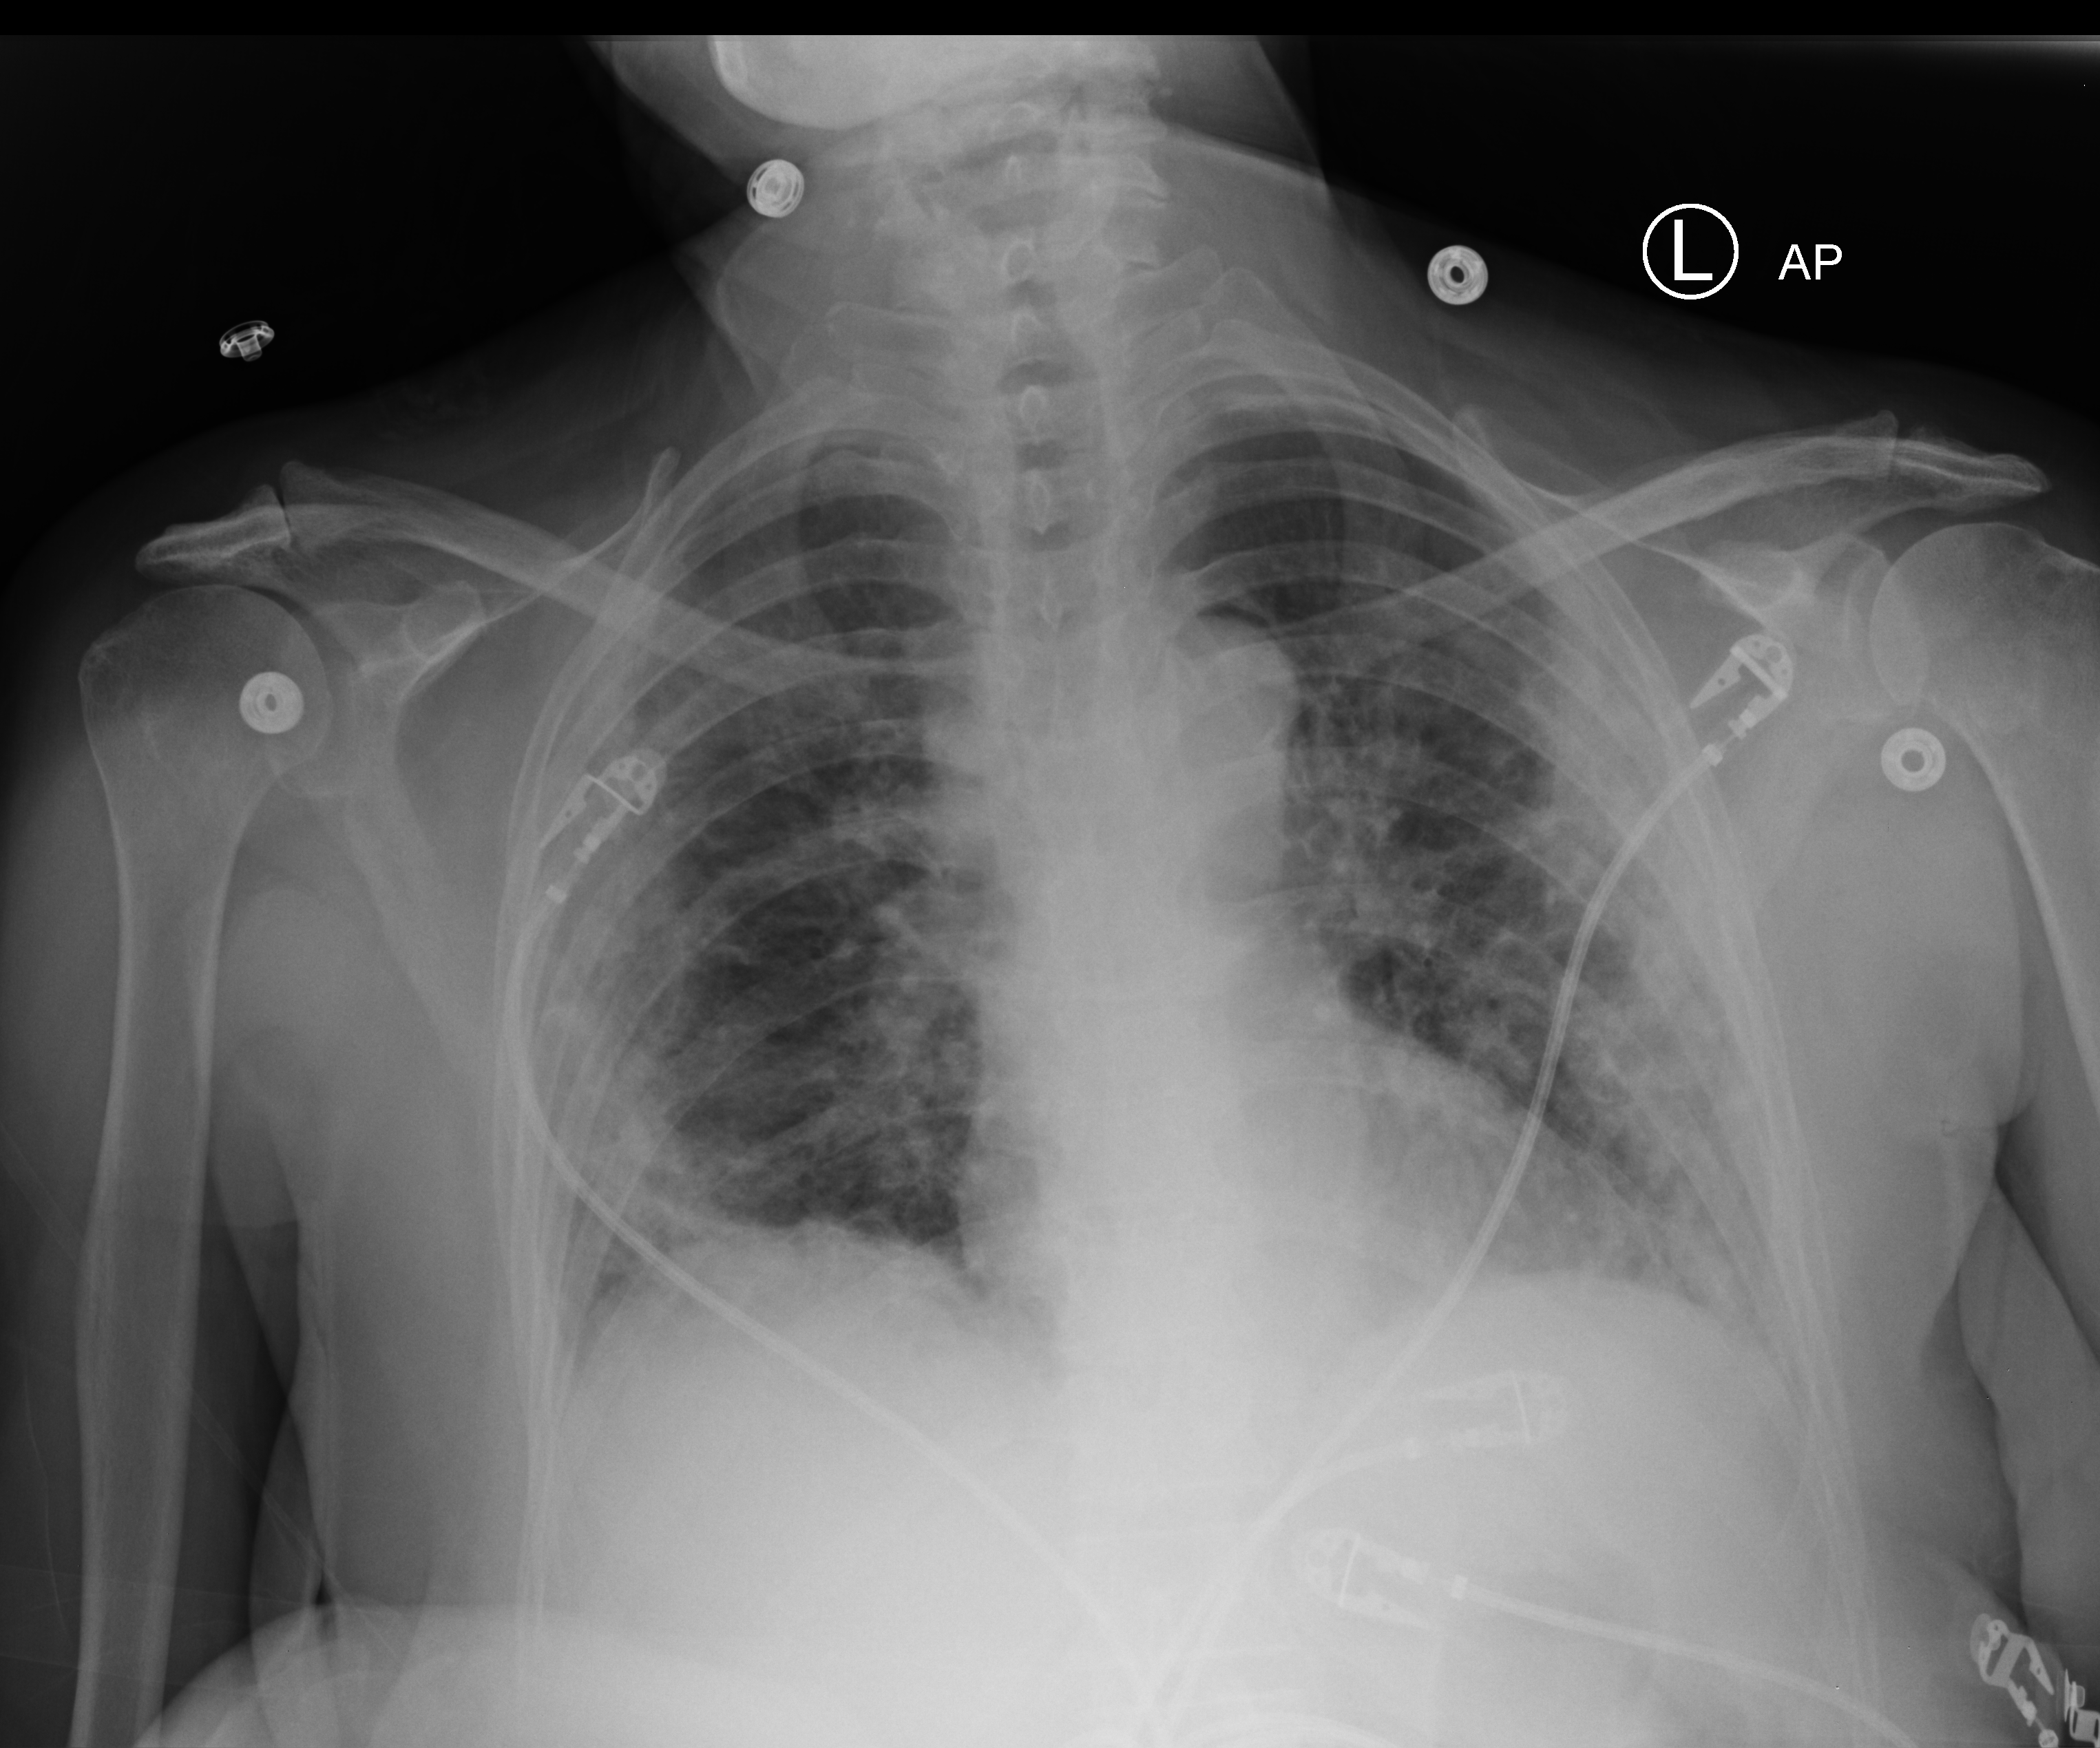
Chest X-ray (portable); anteroposterior (AP) projection. Female patient hospitalised with COVID-19, age 60–74 years.
Admission-level facts for this patient (not findings on this image; timing relative to this image not recorded):
- COPD (admission record): no